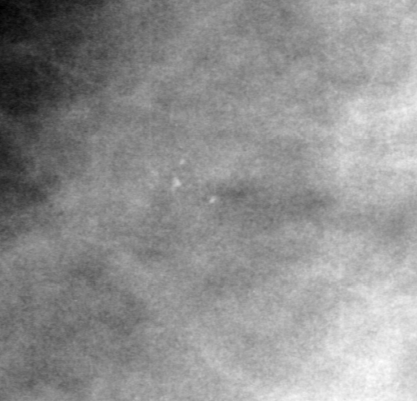
Region of interest cut from a scanned film mammogram (one marked finding), left breast, CC view.
- Finding: calcifications, morphology pleomorphic, distribution clustered; BI-RADS assessment category 4; pathology result (as recorded, not read from the image): benign.